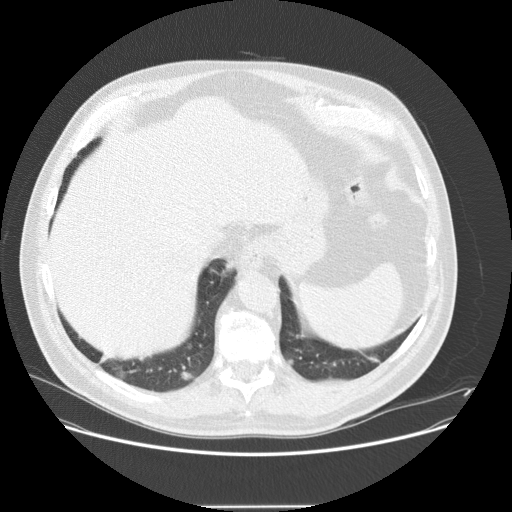
Chest CT (low-dose screening protocol), one axial image; first (baseline) screen; lung window (W 1500 / L -600 HU); 2.5 mm slice thickness; slice 108 of 143 in the series; 512 × 512 image matrix. Male, age 61 years at enrolment. Current smoker at enrolment.
• 3 expert reader's lesion annotations on this slice (largest first), box from (x=91, y=340) to (x=148, y=391) px; (x=197, y=248)–(x=245, y=294); (x=166, y=358)–(x=205, y=395).
• The screening reader recorded 2 non-calcified nodules or masses ≥4 mm on this exam; which of them these boxes mark is not recorded.
• Official screen result: positive, change unspecified: nodule(s) >= 4 mm or enlarging nodule(s), mass(es), or other non-specific abnormalities suspicious for lung cancer.
• Later outcome: lung cancer diagnosed 41 days after this screen — bronchiolo-alveolar carcinoma, mucinous, right lower lobe, well differentiated (G1), stage IV (AJCC 6th edition), 23 mm at pathology.